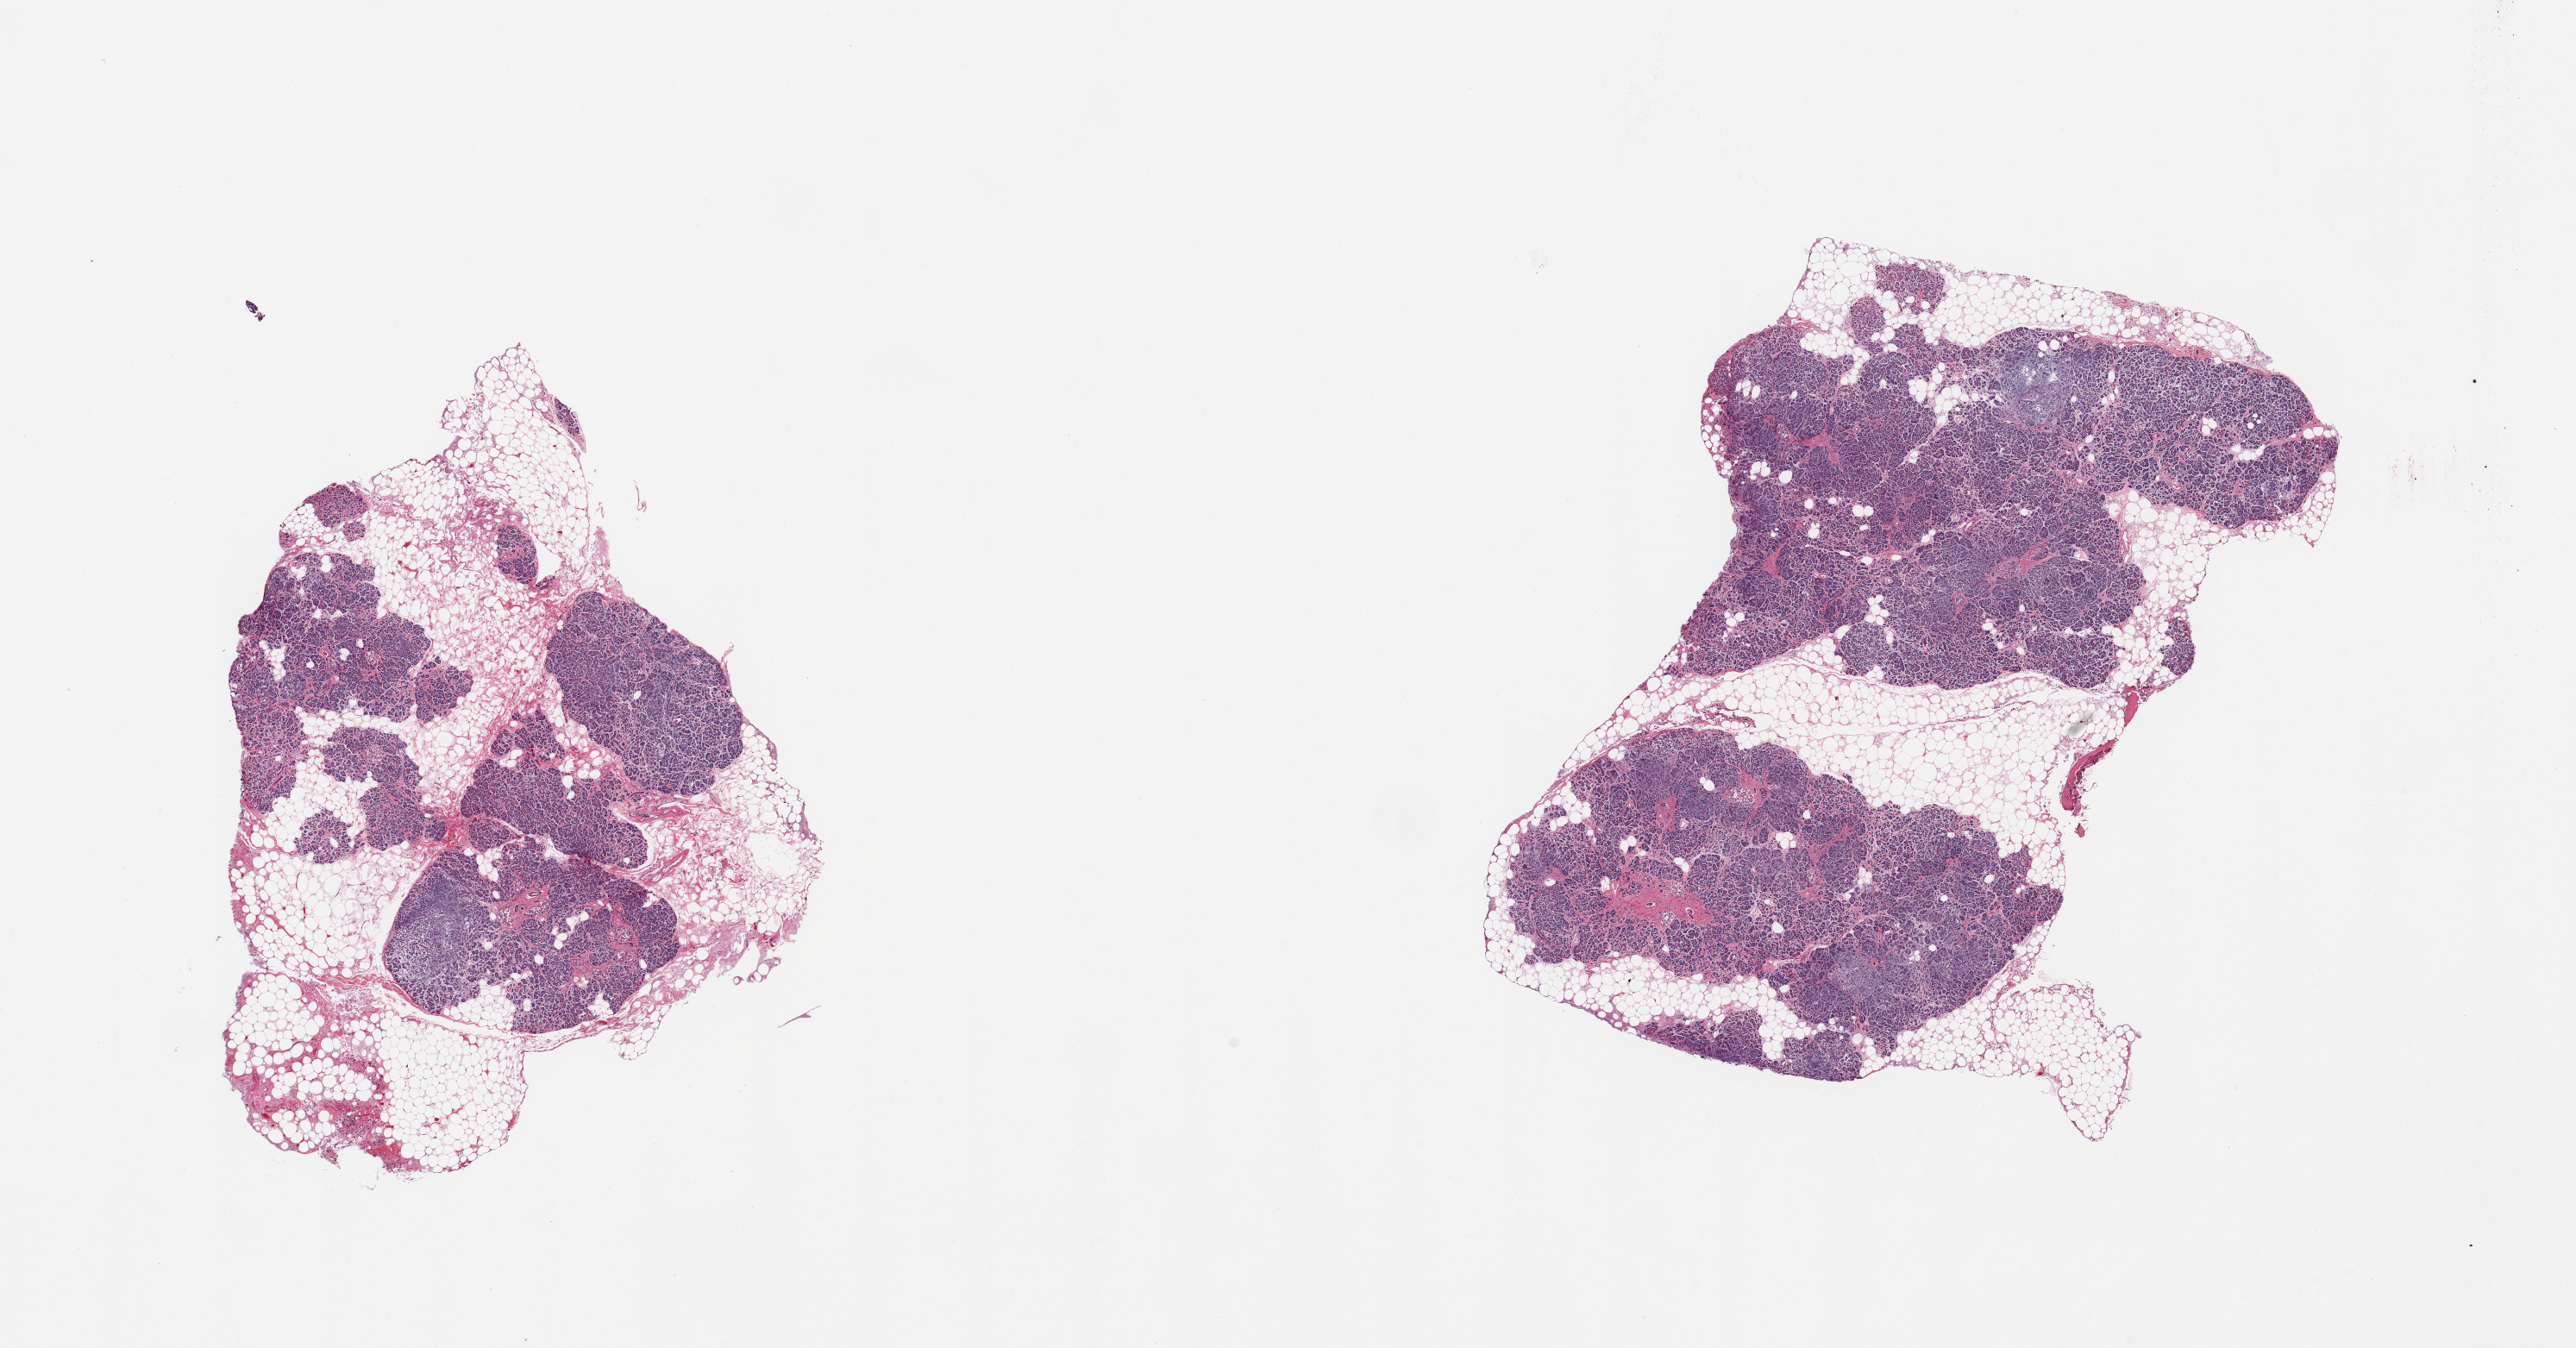
H&E whole-slide image, brightfield, low-resolution overview of the scanned area, about 23.6 x 12.4 mm (acquisition: 20x scan); PAXgene-fixed paraffin-embedded (PFPE) section; section of pancreas (target tissue); donor tissue sample.
* pathologist's review note for this sample: 2 pieces, moderately advanced saponification; ~40% adherent/interstitial adipose tissue